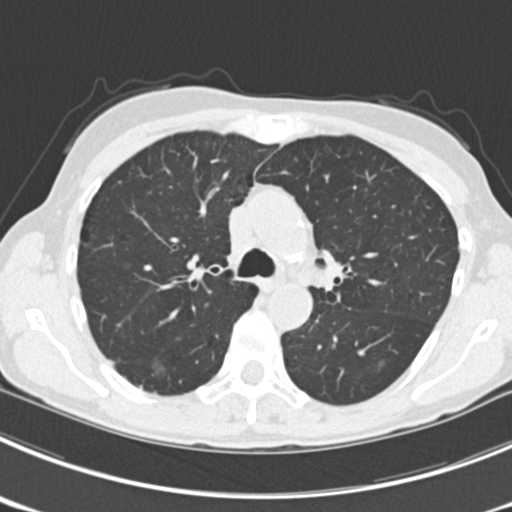
Chest CT (low-dose screening protocol), one axial image. Third screening round (two years after baseline). Lung window (W 1500 / L -600 HU). Standard (soft-tissue) reconstruction kernel (B30f). Slice 70 of 225 in the series. 512 × 512 image matrix, field of view 302 × 302 mm. Female, age 63 years at enrolment. Current smoker at enrolment.
• Expert-annotated lung lesion, box from (x=144, y=349) to (x=181, y=387) px.
• The screening reader recorded 9 non-calcified nodules or masses ≥4 mm on this exam (left upper lobe, right upper lobe, left upper lobe, left lower lobe, right middle lobe, left lower lobe, left lower lobe, right lower lobe, right lower lobe); which of them this box marks is not recorded.